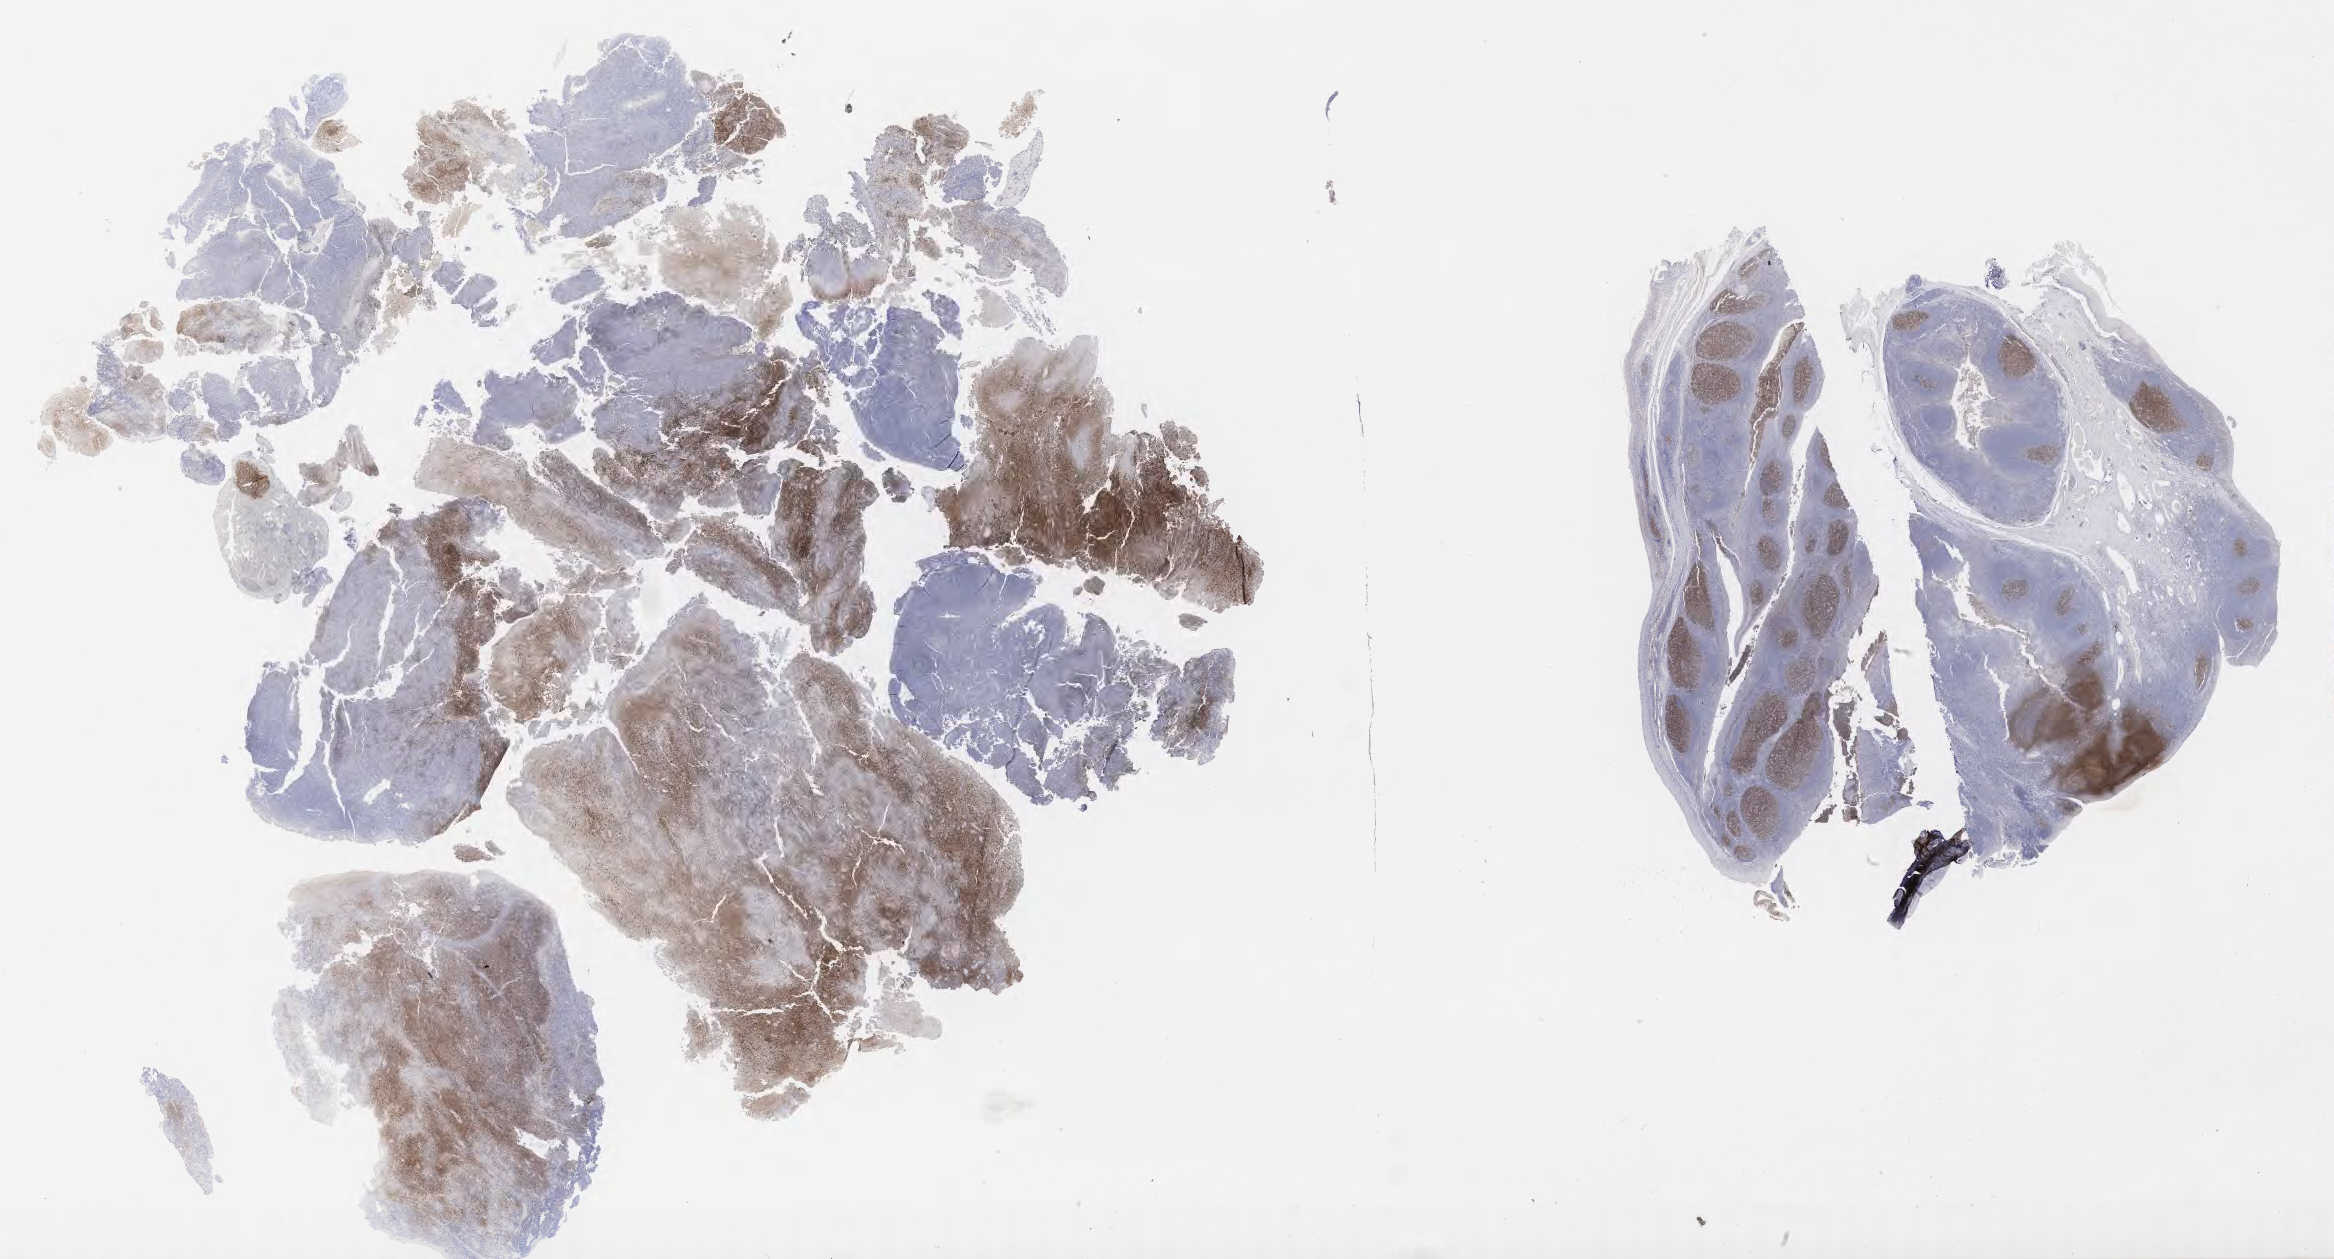
Whole-slide image, immunohistochemical stain for CD10, low-resolution overview of the scanned area, about 37.7 x 20.4 mm, tumor tissue. Patient: male, 47 years old.
Histologic diagnosis: Diffuse large B-cell lymphoma, NOS.